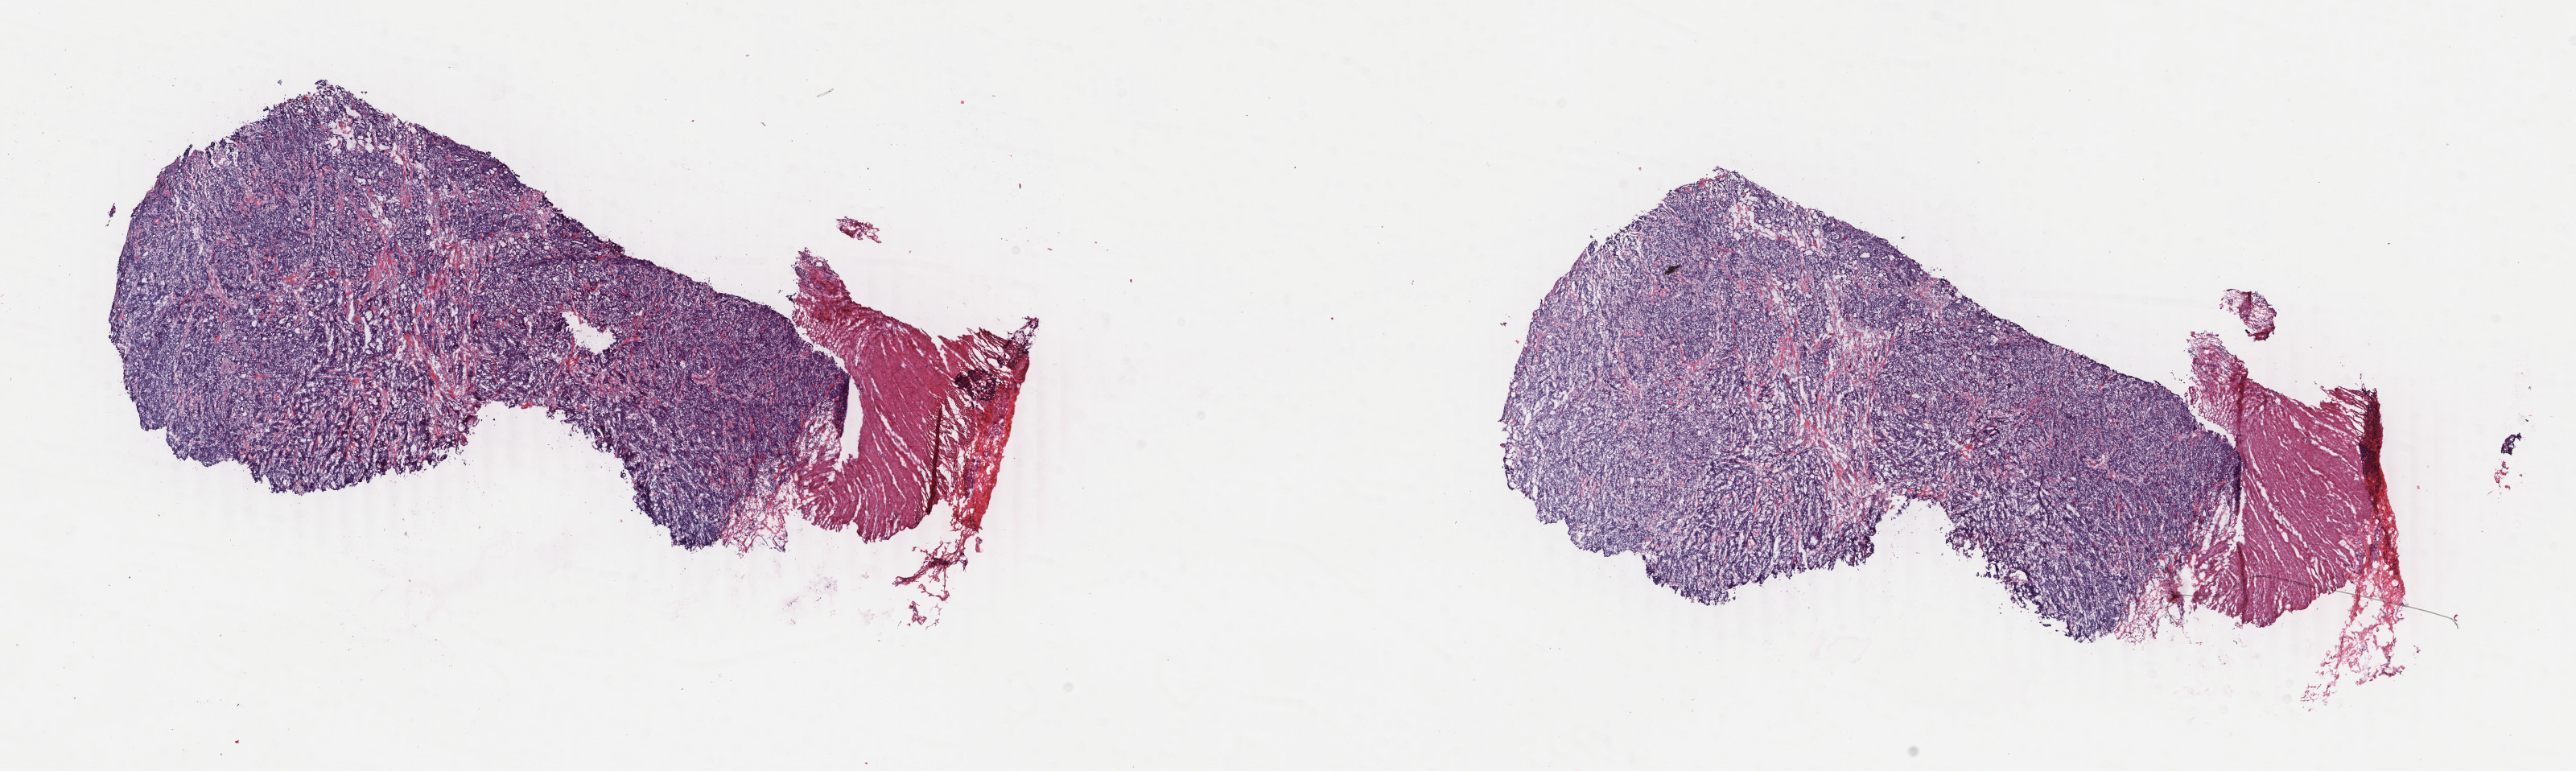
Digitized H&E tissue section (whole slide), shown as a low-resolution overview of the whole scanned area (about 25.5 x 7.6 mm), frozen section from the bottom of the tissue portion, colon, primary tumour sample. Patient: male, age at initial diagnosis 47 years. Composition of this section per pathologist review: tumour cells 80%, tumour nuclei 80%.
Histologic diagnosis: Mucinous adenocarcinoma.